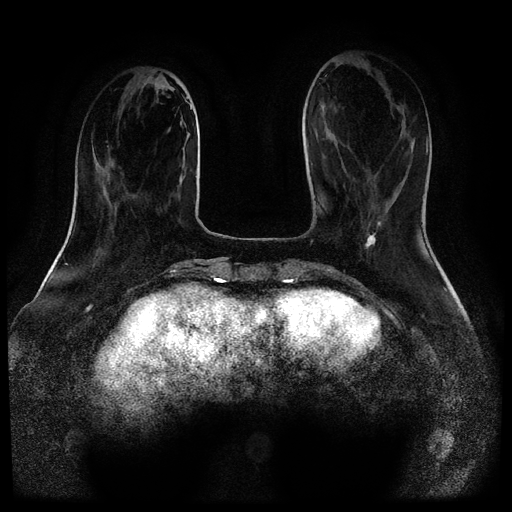
Breast MRI (dynamic contrast-enhanced, multi-phase), one axial slice; slice 31 of 116 in the series (ordered by position); dynamic contrast-enhanced series, time point 2 of 5 at this slice position (early post-contrast); 1.5 T; TE 2.6 ms, TR 5.3 ms; 2 mm slice thickness; 512 × 512 image matrix. Female patient, age 52 years.
Annotated regions visible in this slice (semi-automatically segmented with operator editing):
- breast lesion (labelled 'tumour' in the annotation; benign lesions carry a separate 'benign' label): box from (x=365, y=222) to (x=381, y=248) px